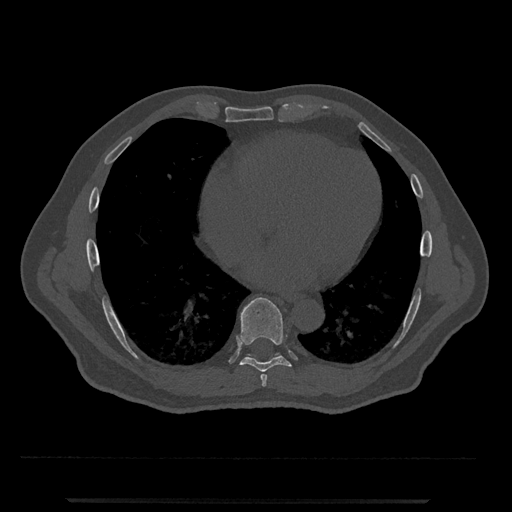
CT including the spine, one axial slice. Slice 622 of 797 in the series (ordered by position). Reconstruction kernel Br40s/3. Bone window (W 1800 / L 400 HU). 512 × 512 image matrix, field of view 419 × 419 mm. Patient: male, 63 years. From the clinical record (not read from this slice): primary cancer: prostate.
Annotated regions visible in this slice (semi-automatic segmentation, software-assisted and operator-edited):
- T7 vertebra: bounding box [x1, y1, x2, y2] px = [260, 374, 267, 387]
- T8 vertebra: [240, 297, 292, 372]
- T9 vertebra: [247, 353, 279, 358]